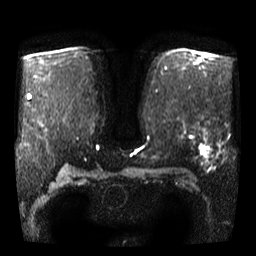
Breast MRI, one axial slice; position 27 of 46 along the scan axis; diffusion-weighted series; image 2 of 4 stored at this slice position (different b-values; order by instance number); 3 T; 5 mm slice thickness; 256 × 256 image matrix, field of view 340 × 340 mm. Female patient.
Structures marked on this image (manually delineated by an expert):
- tumour on diffusion-weighted imaging: bounding box (x1, y1, x2, y2) in pixels: (199, 144, 208, 156)